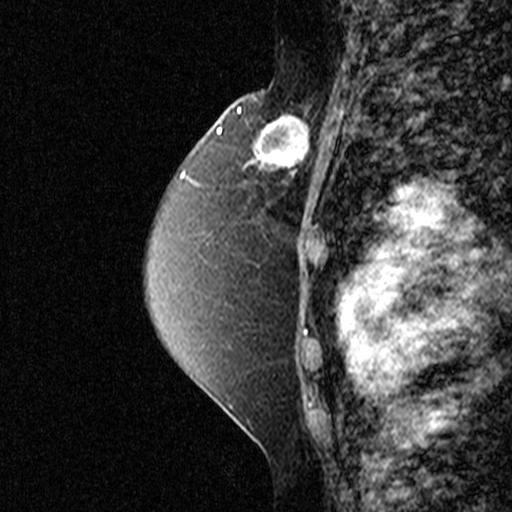
Breast MRI (dynamic contrast-enhanced), one sagittal slice; position 29 of 44 along the scan axis; dynamic contrast-enhanced study with each time point stored as its own series, time point 2 of 3 at this slice position (early post-contrast, ordered by acquisition time); 1.5 T; TE 4.5 ms, TR 11 ms; 3 mm slice thickness; 512 × 512 image matrix, field of view 200 × 200 mm. Patient: female, 49 years. From the clinical record (not read from this slice): setting: breast cancer imaged before/during neoadjuvant chemotherapy; receptor status: triple-negative.
Structures marked on this image (semi-automatically segmented with operator editing):
- analysis volume of interest (the breast-tissue region the enhancement analysis was run in; not a lesion): bounding box [x1, y1, x2, y2] px = [245, 100, 335, 197]
- tumour enhancement mask (voxels above the 90 % enhancement threshold inside the analysis volume of interest): [256, 114, 311, 183]